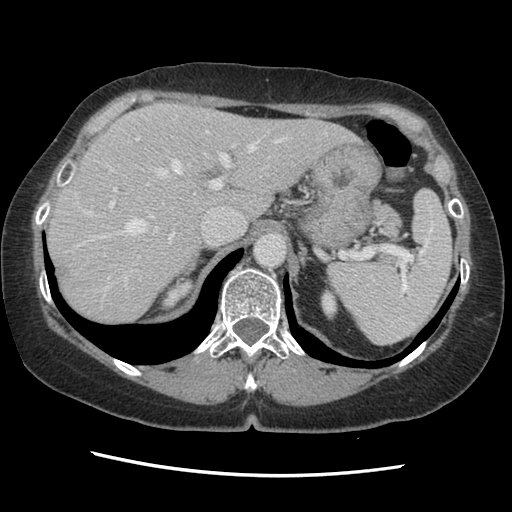
Contrast-enhanced abdominal CT, one axial slice; position 99 of 141 along the scan axis; soft-tissue window (W 400 / L 40 HU); 2.5 mm slice thickness; 512 × 512 image matrix. Female patient, age 61 years. From the clinical record (not read from this slice): diagnosis: colorectal cancer liver metastases, imaged before liver resection; multiple liver metastases: no; largest metastasis: 2.4 cm; chemotherapy before resection: no.
Structures marked on this image (manually delineated by an expert):
- hepatic veins: bounding box (x1, y1, x2, y2) in pixels: (77, 116, 287, 290)
- liver: (45, 104, 353, 326)
- planned liver remnant (the part of the liver to remain after resection): (45, 104, 353, 326)
- portal vein (with intrahepatic branches): (110, 137, 236, 242)